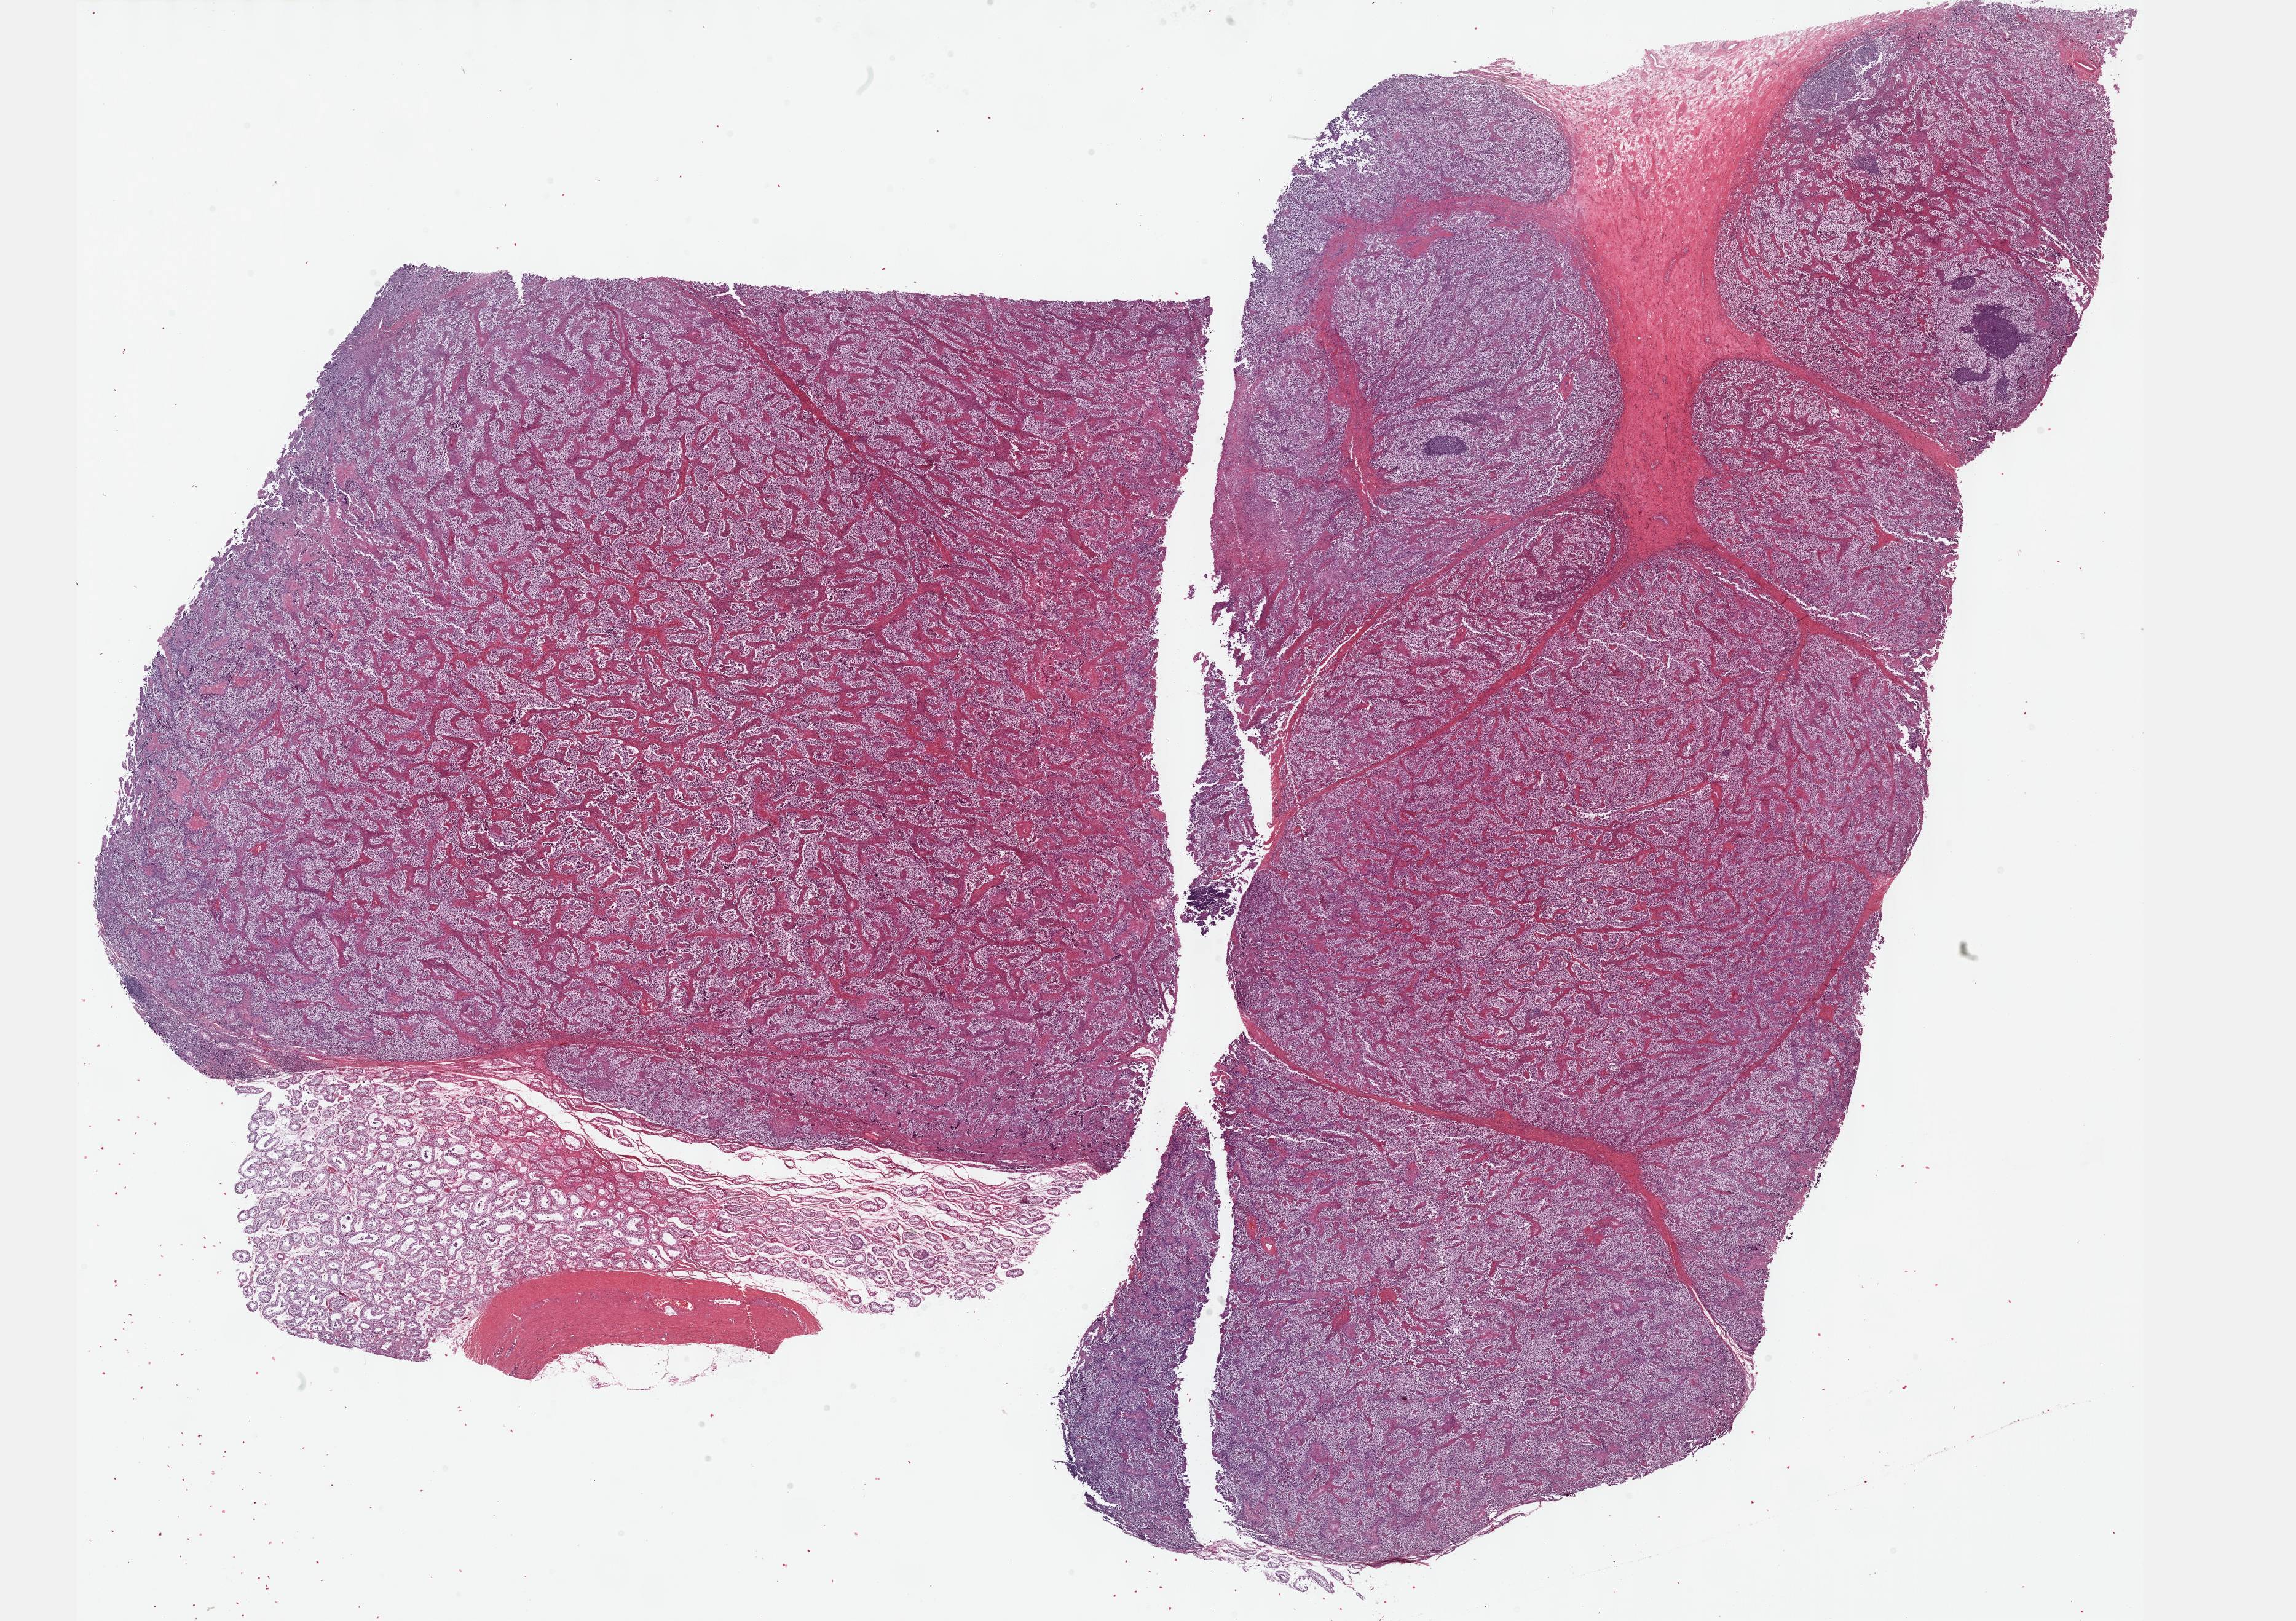
Digitized H&E tissue section (whole slide), low-resolution overview of the scanned area, about 30.2 x 21.3 mm (from a 40x scan). Formalin-fixed paraffin-embedded (FFPE) diagnostic section. Sample: primary tumour, testis. Patient: male, age at initial diagnosis 23 years.
Histologic diagnosis: Seminoma, NOS. TNM: TX NX M0. AJCC pathologic stage: IA (6th edition).